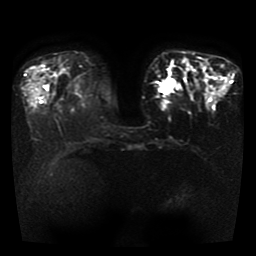
Breast MRI, one axial slice; position 12 of 41 along the scan axis; diffusion-weighted series; image 2 of 4 stored at this slice position (different b-values; order by instance number); 1.5 T; 5 mm slice thickness; 256 × 256 image matrix, field of view 330 × 330 mm. Female patient.
Annotated regions visible in this slice (outlined manually by an expert reader):
- tumour on diffusion-weighted imaging: bounding box <159,79,177,92> (left, top, right, bottom; pixels)